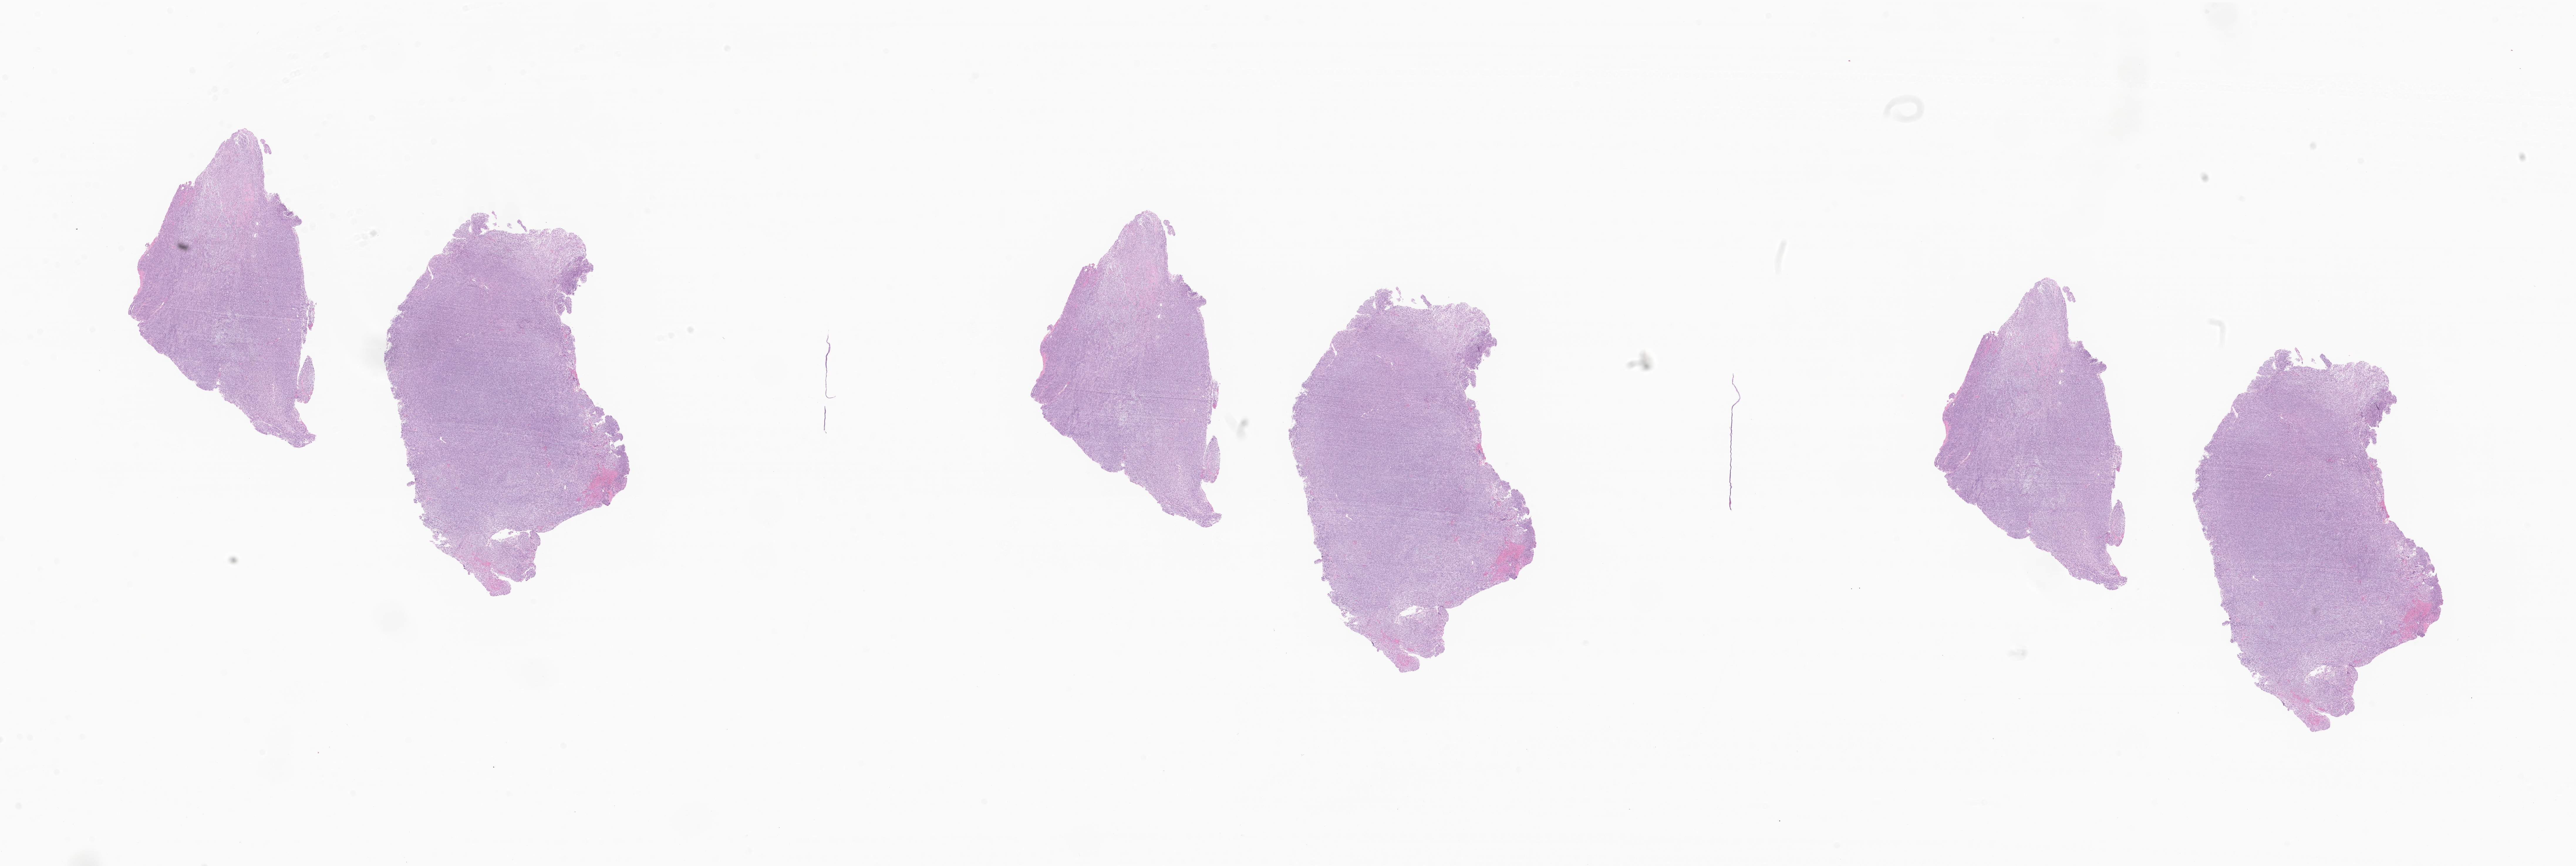
H&E whole-slide image of tumor tissue from the soft tissue of upper extremity, low-resolution overview of the scanned area, about 37.0 x 12.4 mm; formalin-fixed paraffin-embedded section. Patient: male, age 57 months (4 years 9 months).
• diagnosis (ICD-O-3 morphology term): Synovial sarcoma, NOS